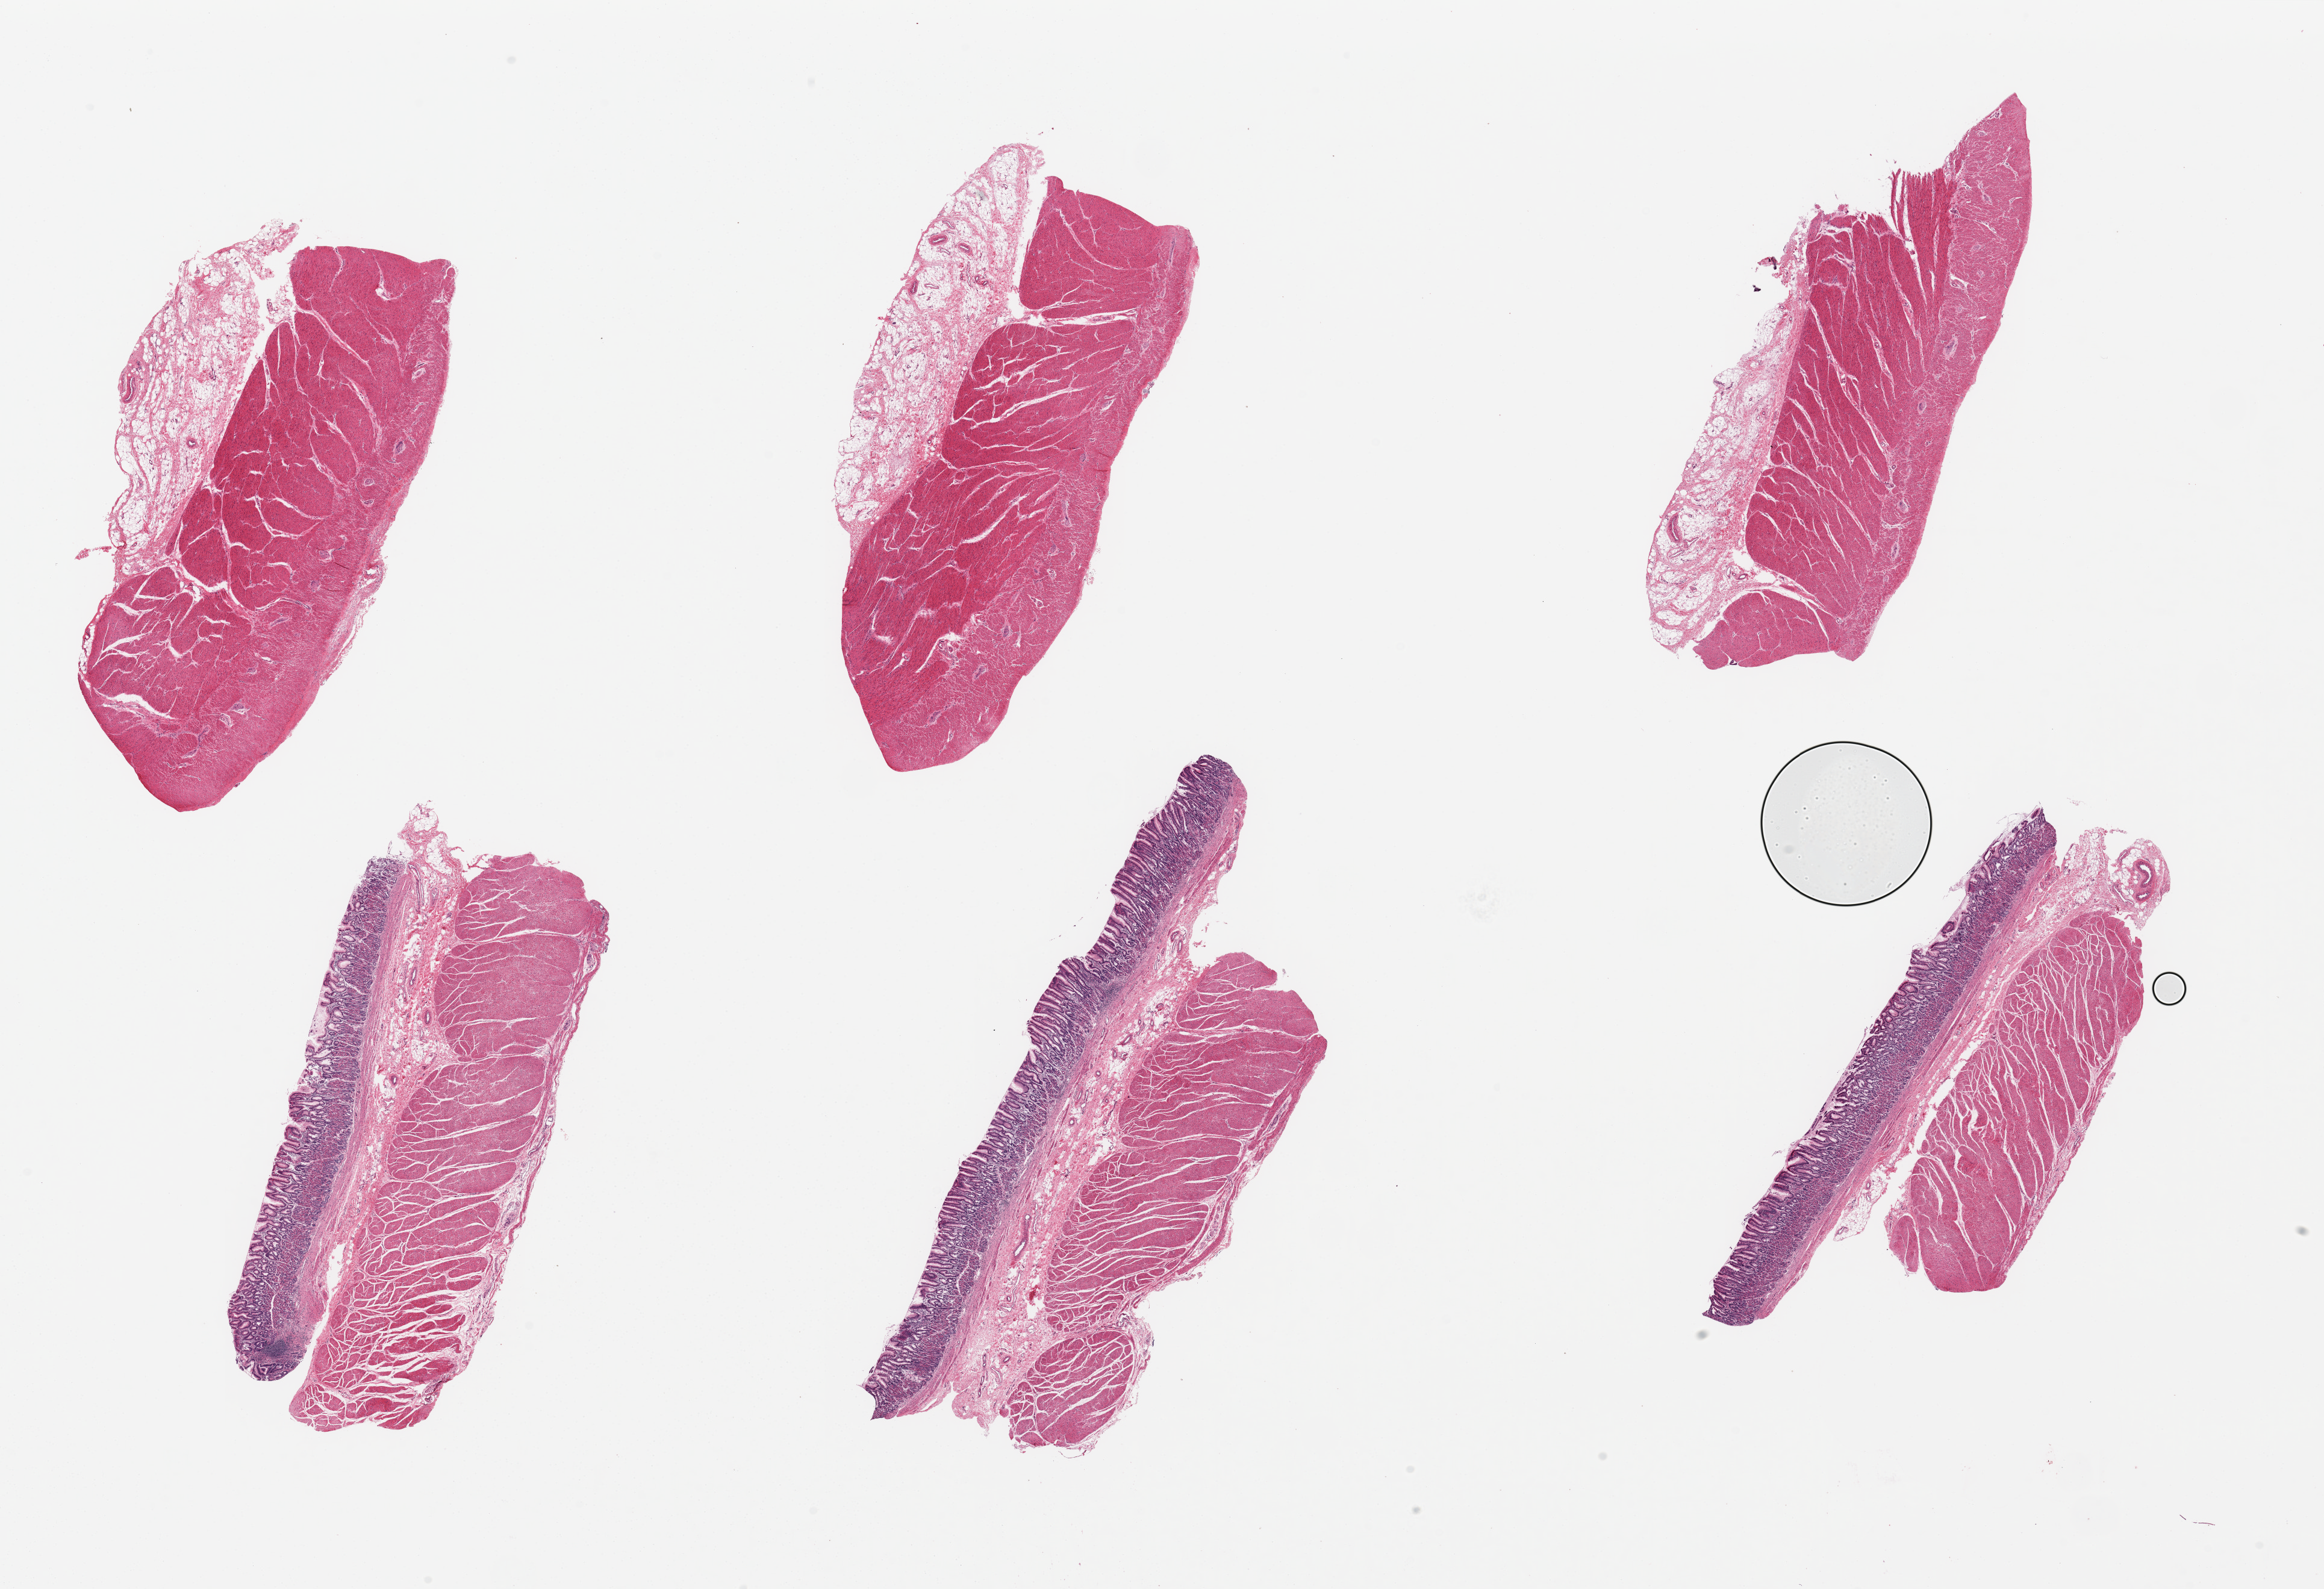
Digitized hematoxylin and eosin (H&E)-stained section, shown as a low-resolution overview of the whole scanned area (about 30.5 x 20.9 mm, slide scanned at 20x); PAXgene-fixed, paraffin-embedded tissue; target tissue: stomach; donor tissue sample. Donor: female.
Pathologist's review note for this sample: 6 pieces, up to 9.5x4mm; 3 are full thickness, other 3 are muscularis only with adjacent submucosal adipose.